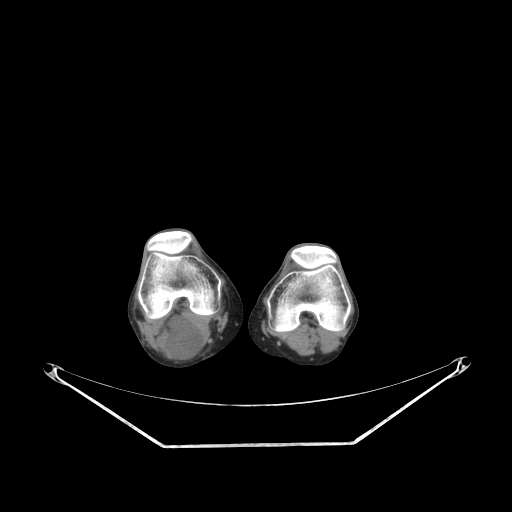
CT of an extremity soft-tissue mass (from a PET/CT study), one axial slice; slice 166 of 267 in the series (ordered by position); reconstruction kernel SOFT; 140 kVp; soft-tissue window (W 400 / L 40 HU); 3.75 mm slice thickness; 512 × 512 image matrix, field of view 500 × 500 mm. Female patient. From the clinical record (not read from this slice): histological type: liposarcoma; site of the primary tumour: right thigh.
Outlined on this slice (expert contour drawn on MRI and transferred to this co-registered scan by the dataset authors):
- gross tumour volume (mass): box from (x=155, y=313) to (x=204, y=359) px